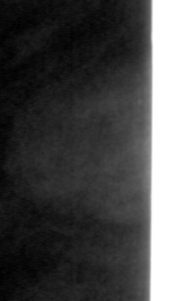
Crop from a digitized film mammogram around one marked abnormality; left breast; CC view; BI-RADS breast density category 3 (scale 1–4).
Finding: mass, shape lobulated, margins circumscribed; BI-RADS assessment category 4; pathology (as recorded): benign.